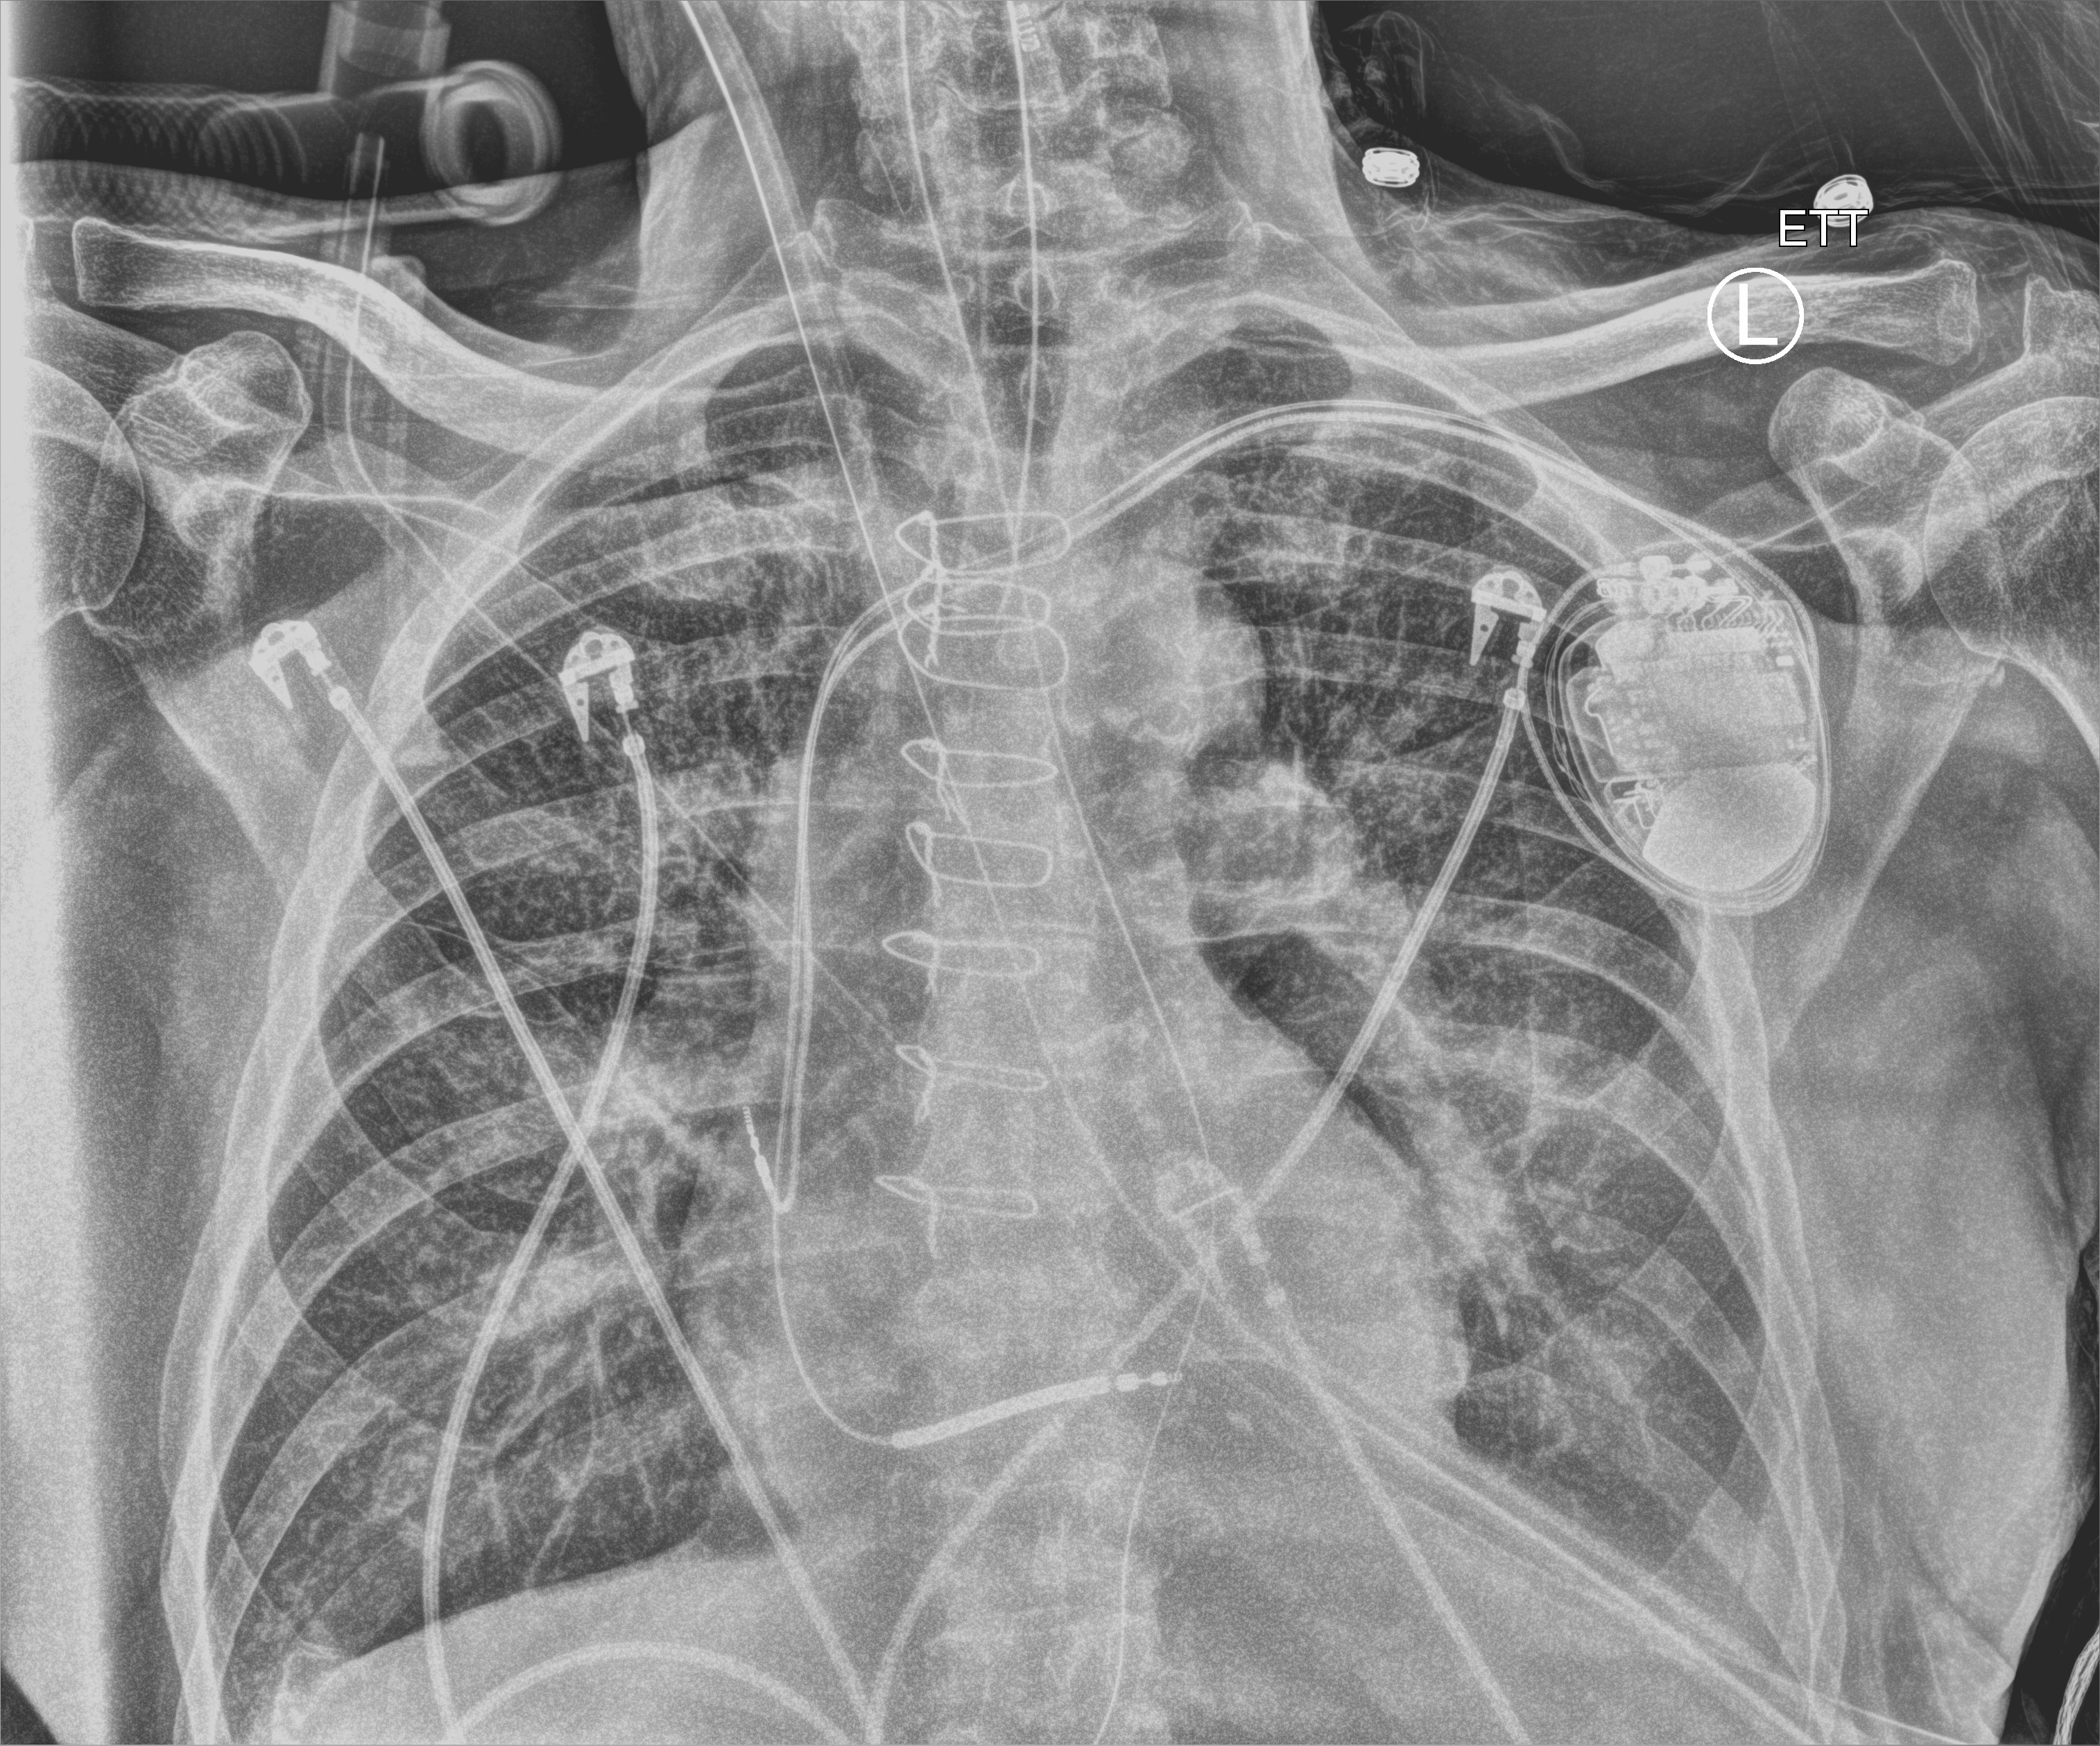
Portable chest radiograph, anteroposterior (AP) projection. Patient hospitalised with COVID-19; male, aged 75–90 years.
From the hospital-stay record, not from the radiograph (when in the stay this image was taken is not recorded): mechanically ventilated during this hospital stay: yes; length of hospital stay: 11 days.